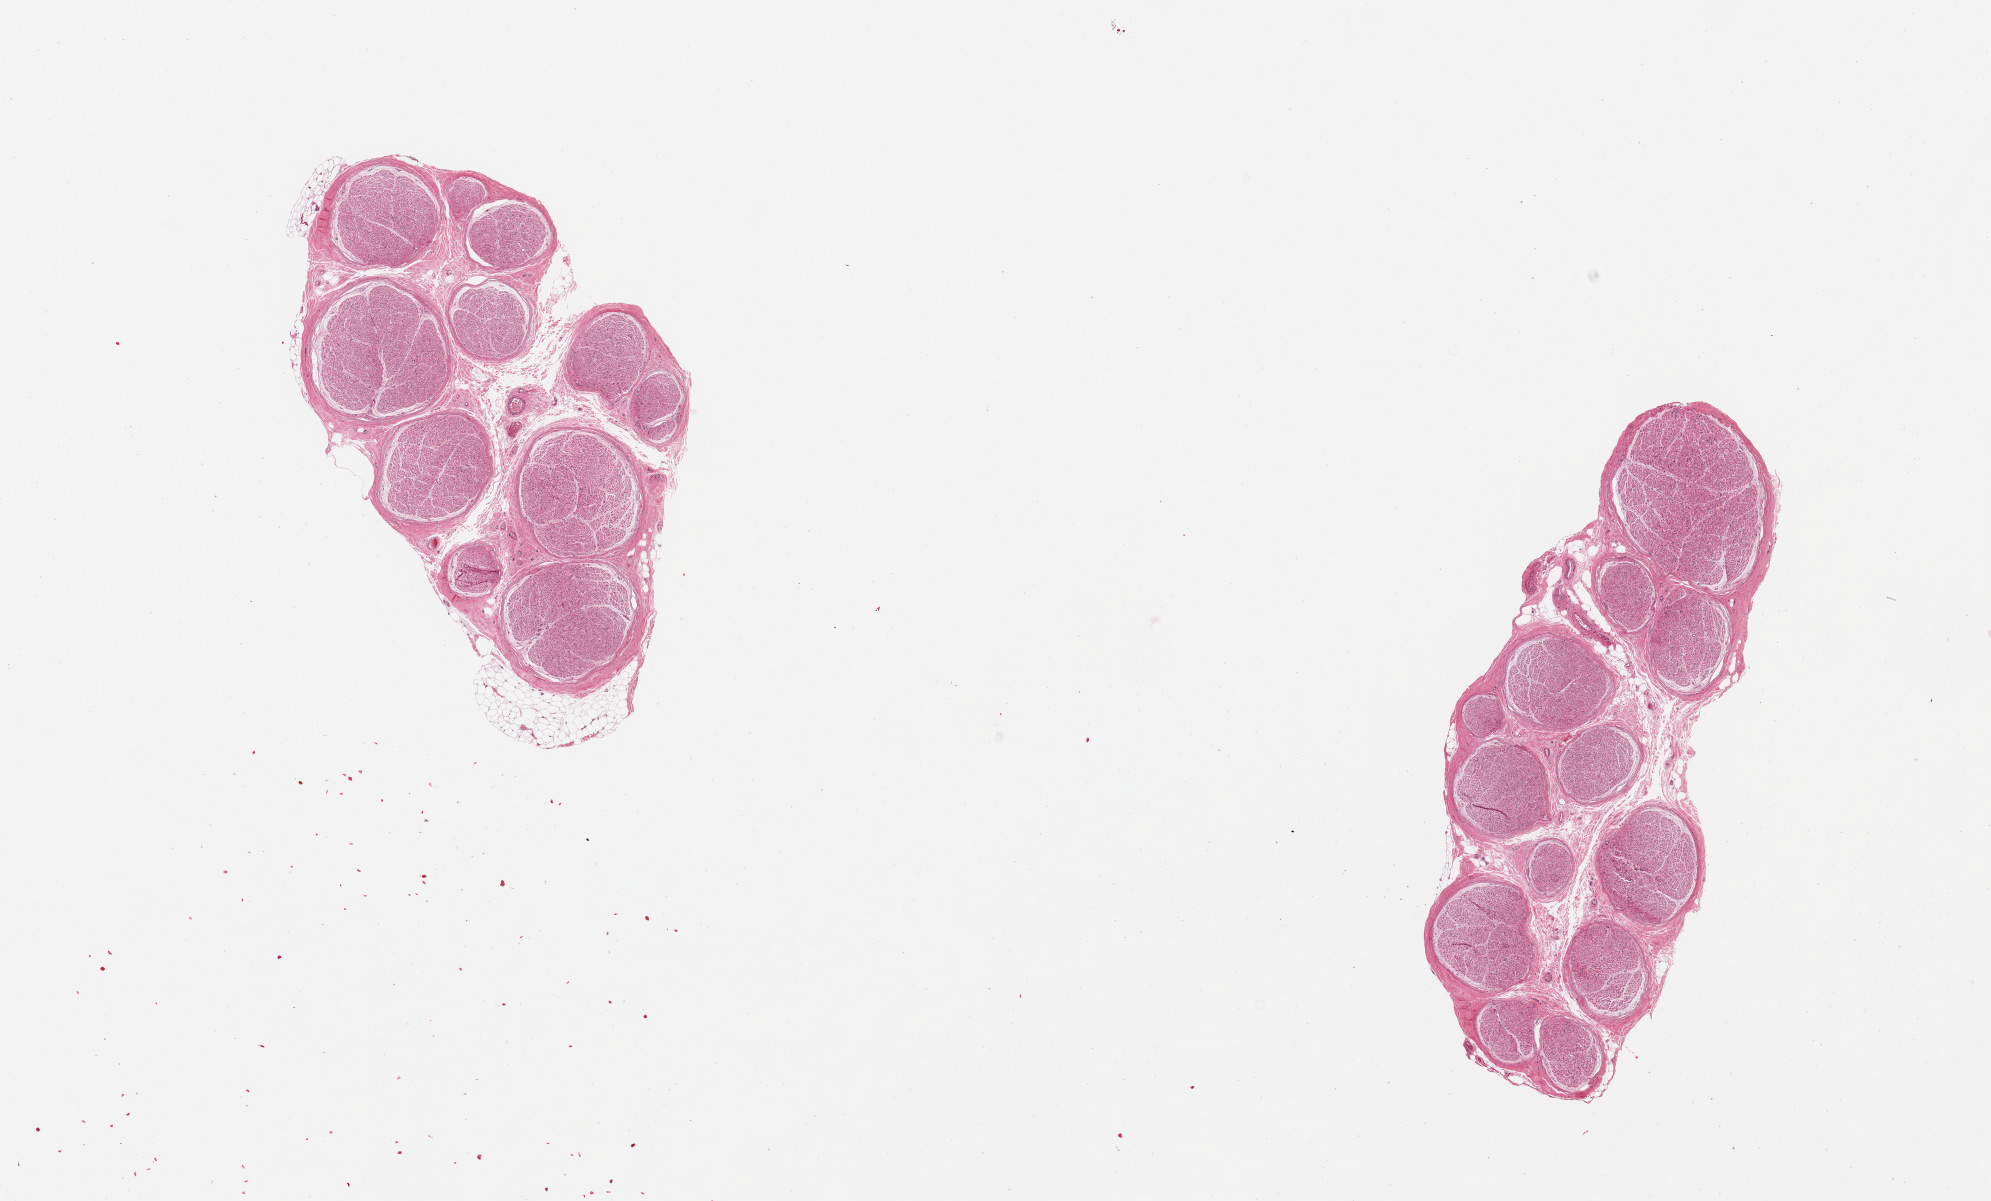
Whole-slide image, haematoxylin and eosin stain, brightfield — a low-resolution overview of the entire scanned area, about 15.8 x 9.5 mm (slide scanned at 20x), PAXgene-fixed, paraffin-embedded tissue, section of tibial nerve (target tissue), donor tissue sample. Donor sex: female.
* review note (as recorded): 2 pieces; <5% internal fat